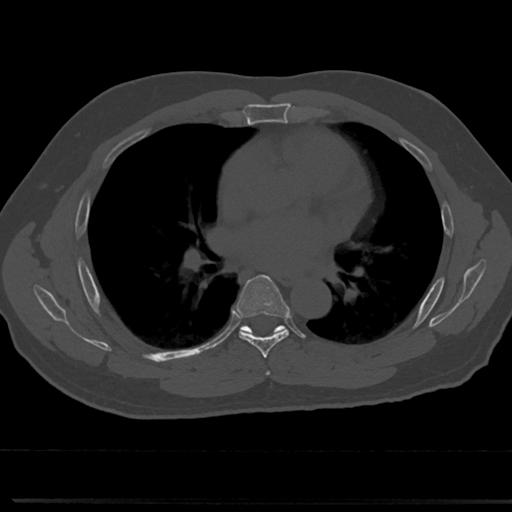
CT including the spine, one axial slice; slice 441 of 817 in the series (ordered by position); reconstruction kernel Br40s/3; bone window (W 1800 / L 400 HU); 0.5 mm slice thickness; 512 × 512 image matrix, field of view 355 × 355 mm. Male patient, age 61 years. From the clinical record (not read from this slice): primary cancer: prostate.
Annotated regions visible in this slice (semi-automatically segmented with operator editing):
- T5 vertebra: bounding box (x1, y1, x2, y2) in pixels: (264, 359, 273, 377)
- T6 vertebra: (222, 277, 309, 352)